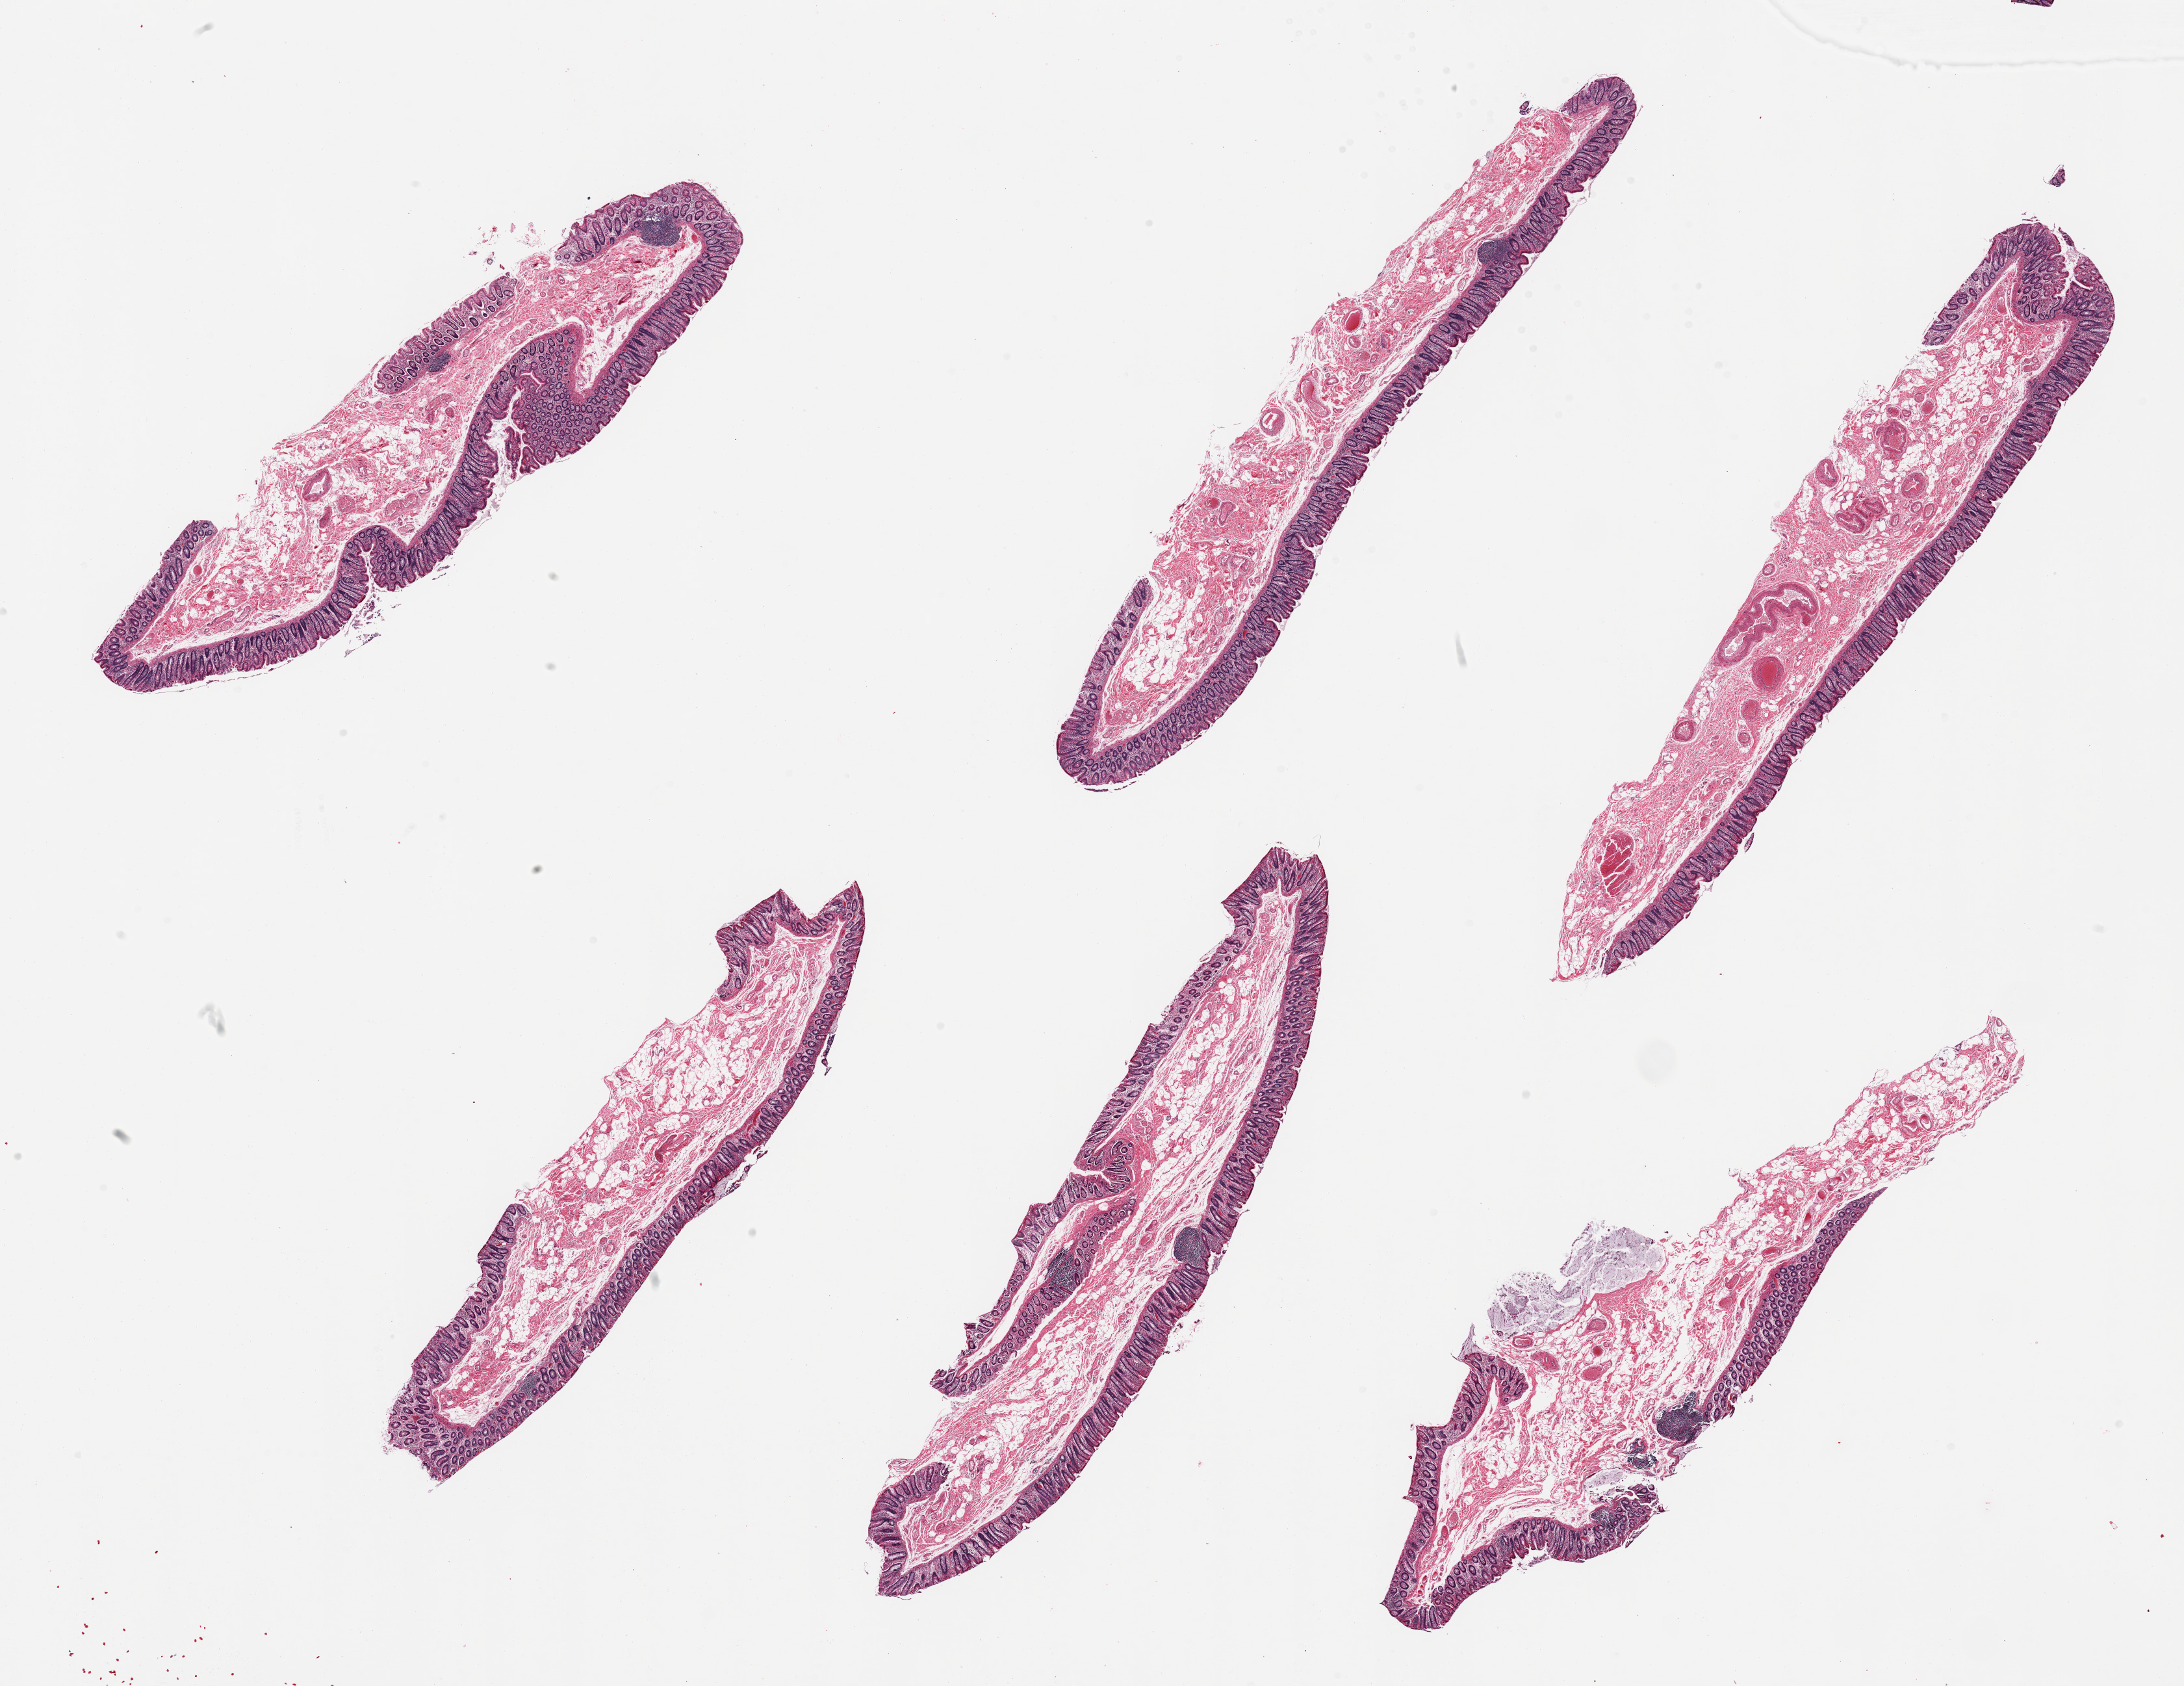
H&E whole-slide image, brightfield, low-resolution overview of the scanned area, about 26.6 x 20.5 mm. PAXgene-fixed, paraffin-embedded tissue. Sampled site (target tissue): transverse colon. Tissue donor sample. Donor sex: female.
• pathologist's review note for this sample: 6 pieces, mucosa well preserved, ~0.2-0.3mm, ~25% thickness